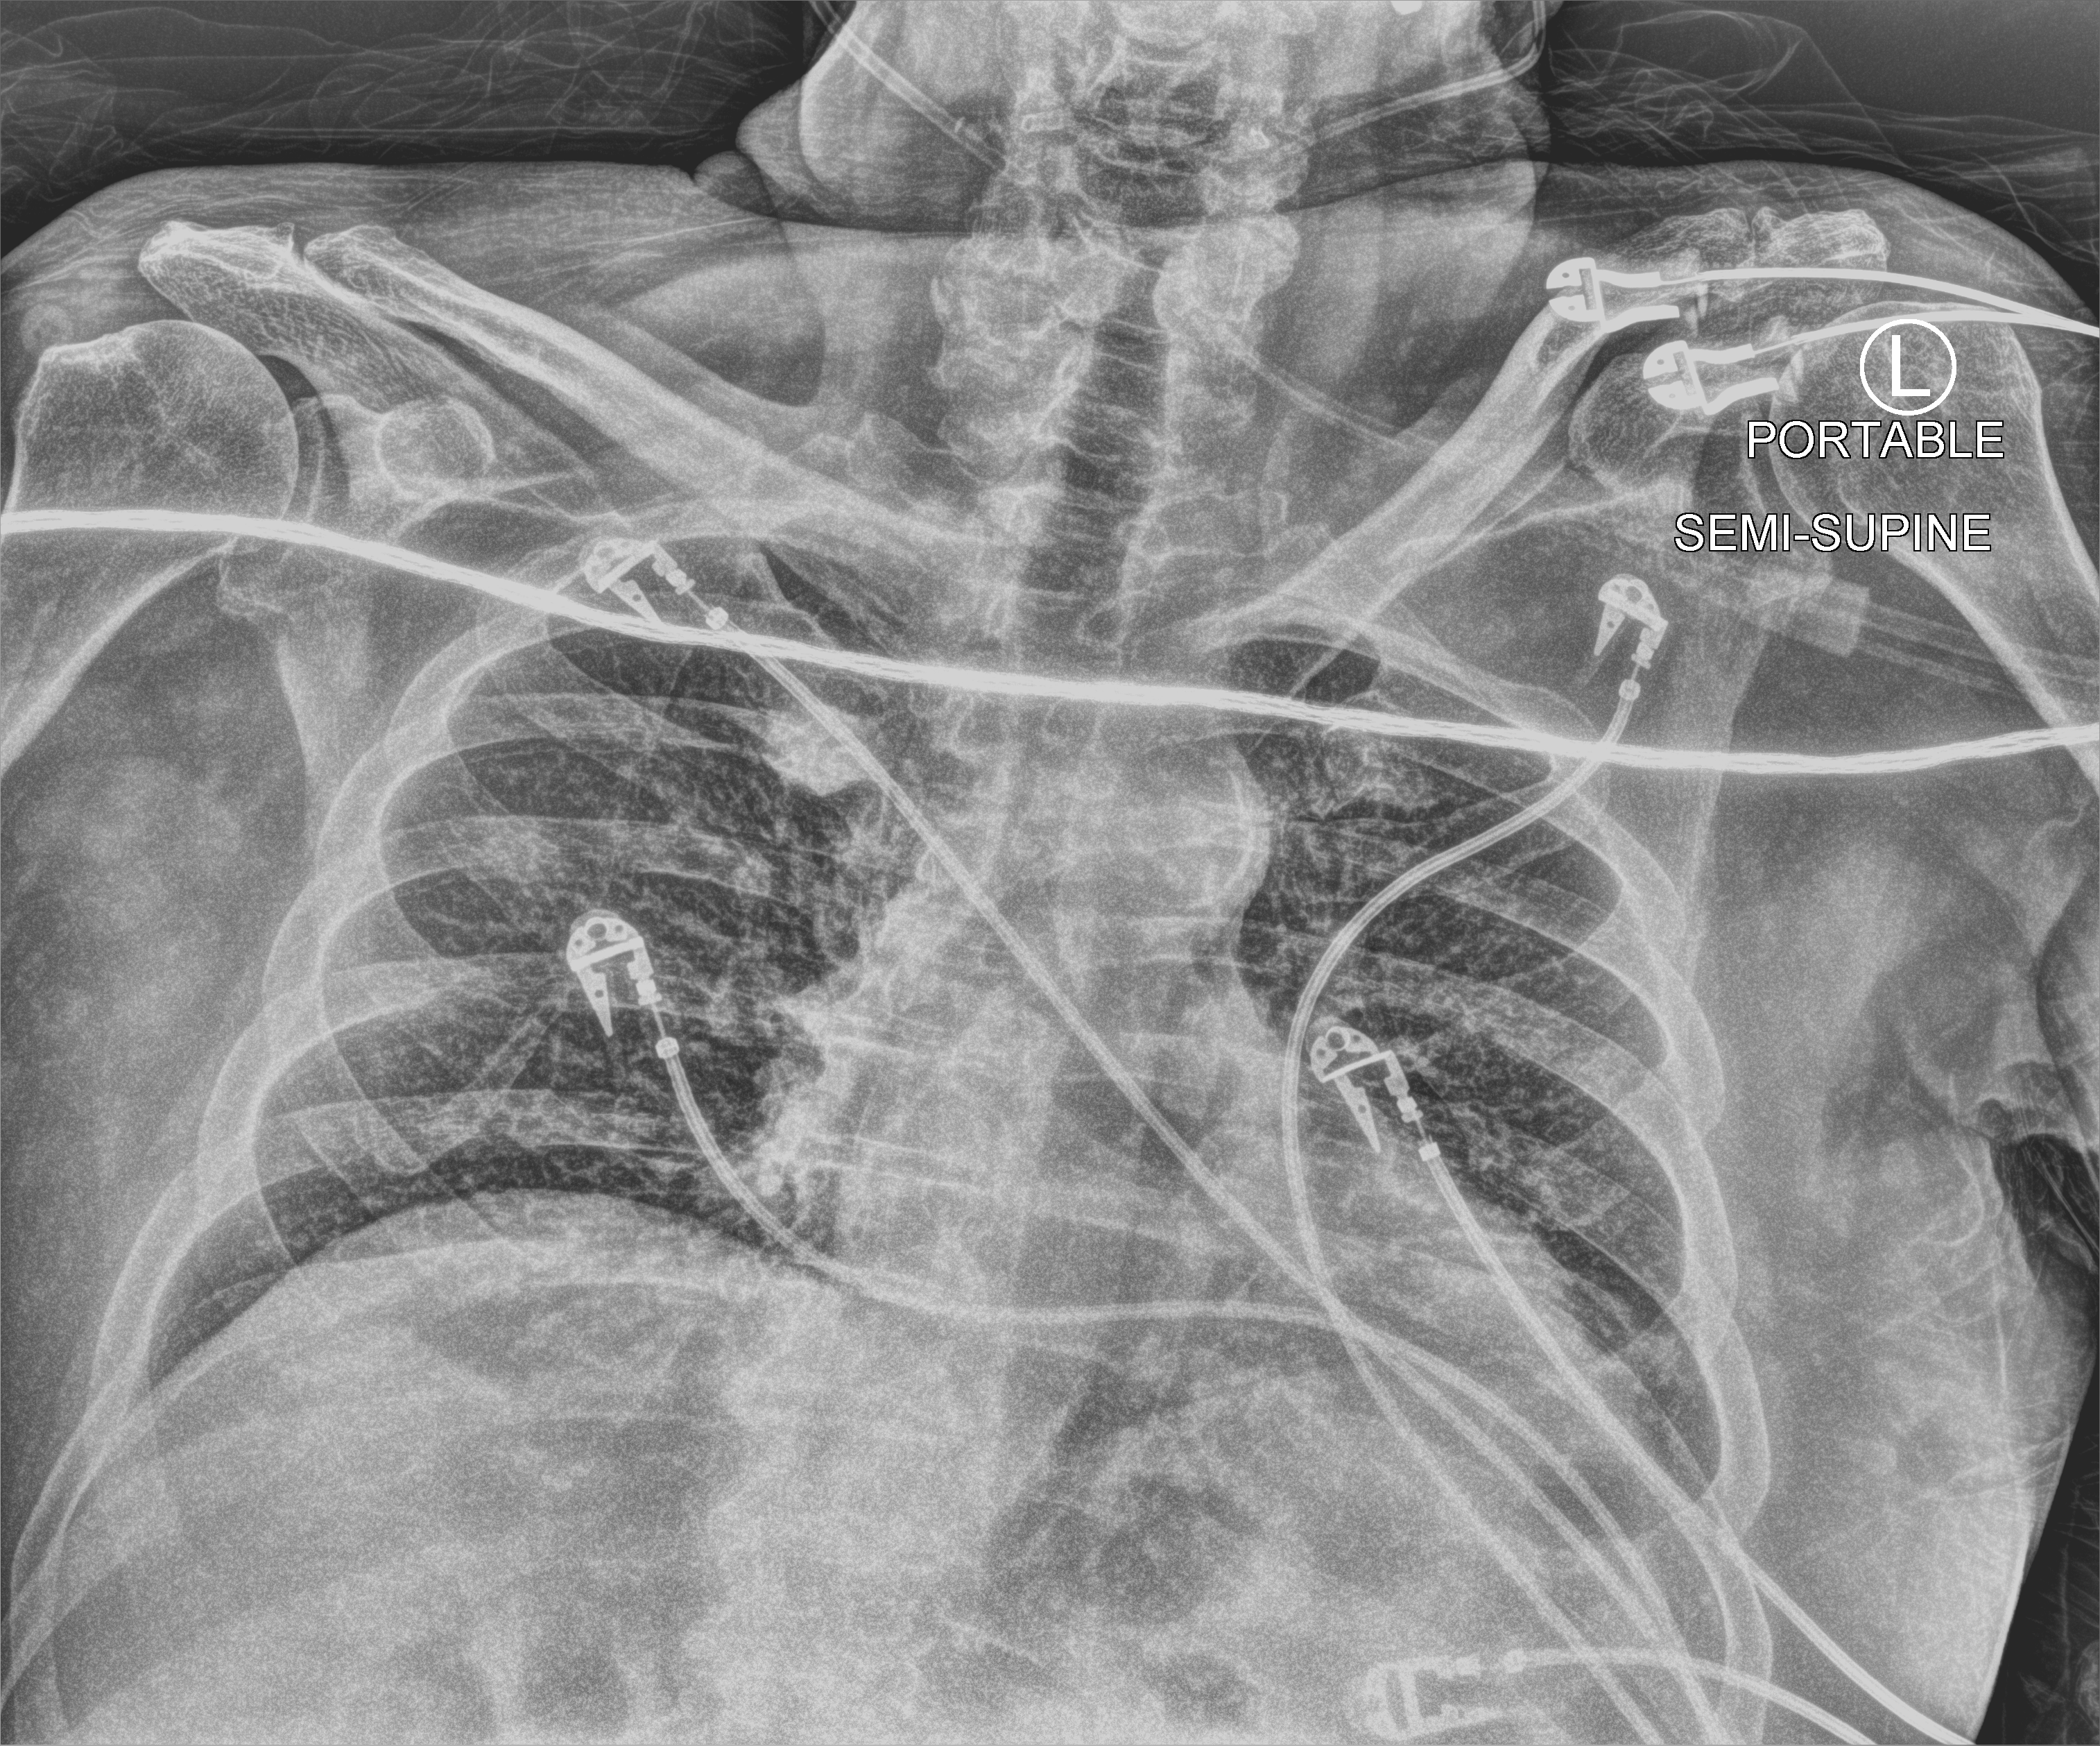
Bedside chest radiograph (computed radiography), anteroposterior (AP) projection. Male patient hospitalised with COVID-19, age 75–90 years.
From the hospital-stay record, not from the radiograph (when in the stay this image was taken is not recorded): length of hospital stay: 32 days; chronic kidney disease (admission record): no; admitted to intensive care during this hospital stay: no.